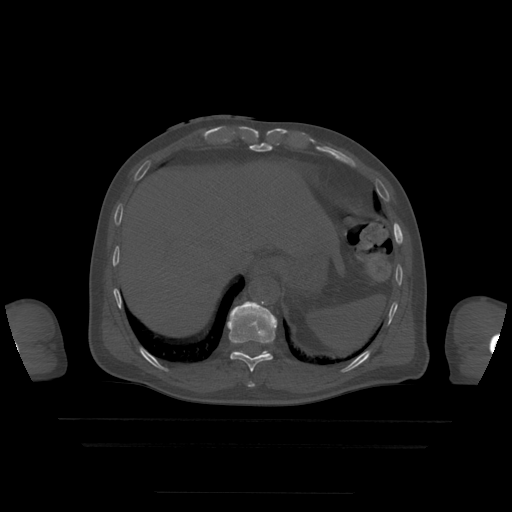
CT including the spine, one axial slice. Position 237 of 522 along the scan axis. Bone window (W 1800 / L 400 HU). 1.25 mm slice thickness. 512 × 512 image matrix, field of view 436 × 436 mm. Patient age 68 years. From the clinical record (not read from this slice): primary cancer: urothelial.
Annotated regions visible in this slice (semi-automatic segmentation, software-assisted and operator-edited):
- T10 vertebra: bounding box (x1, y1, x2, y2) in pixels: (227, 302, 278, 372)
- T11 vertebra: (262, 351, 266, 354)
- T9 vertebra: (248, 383, 255, 387)